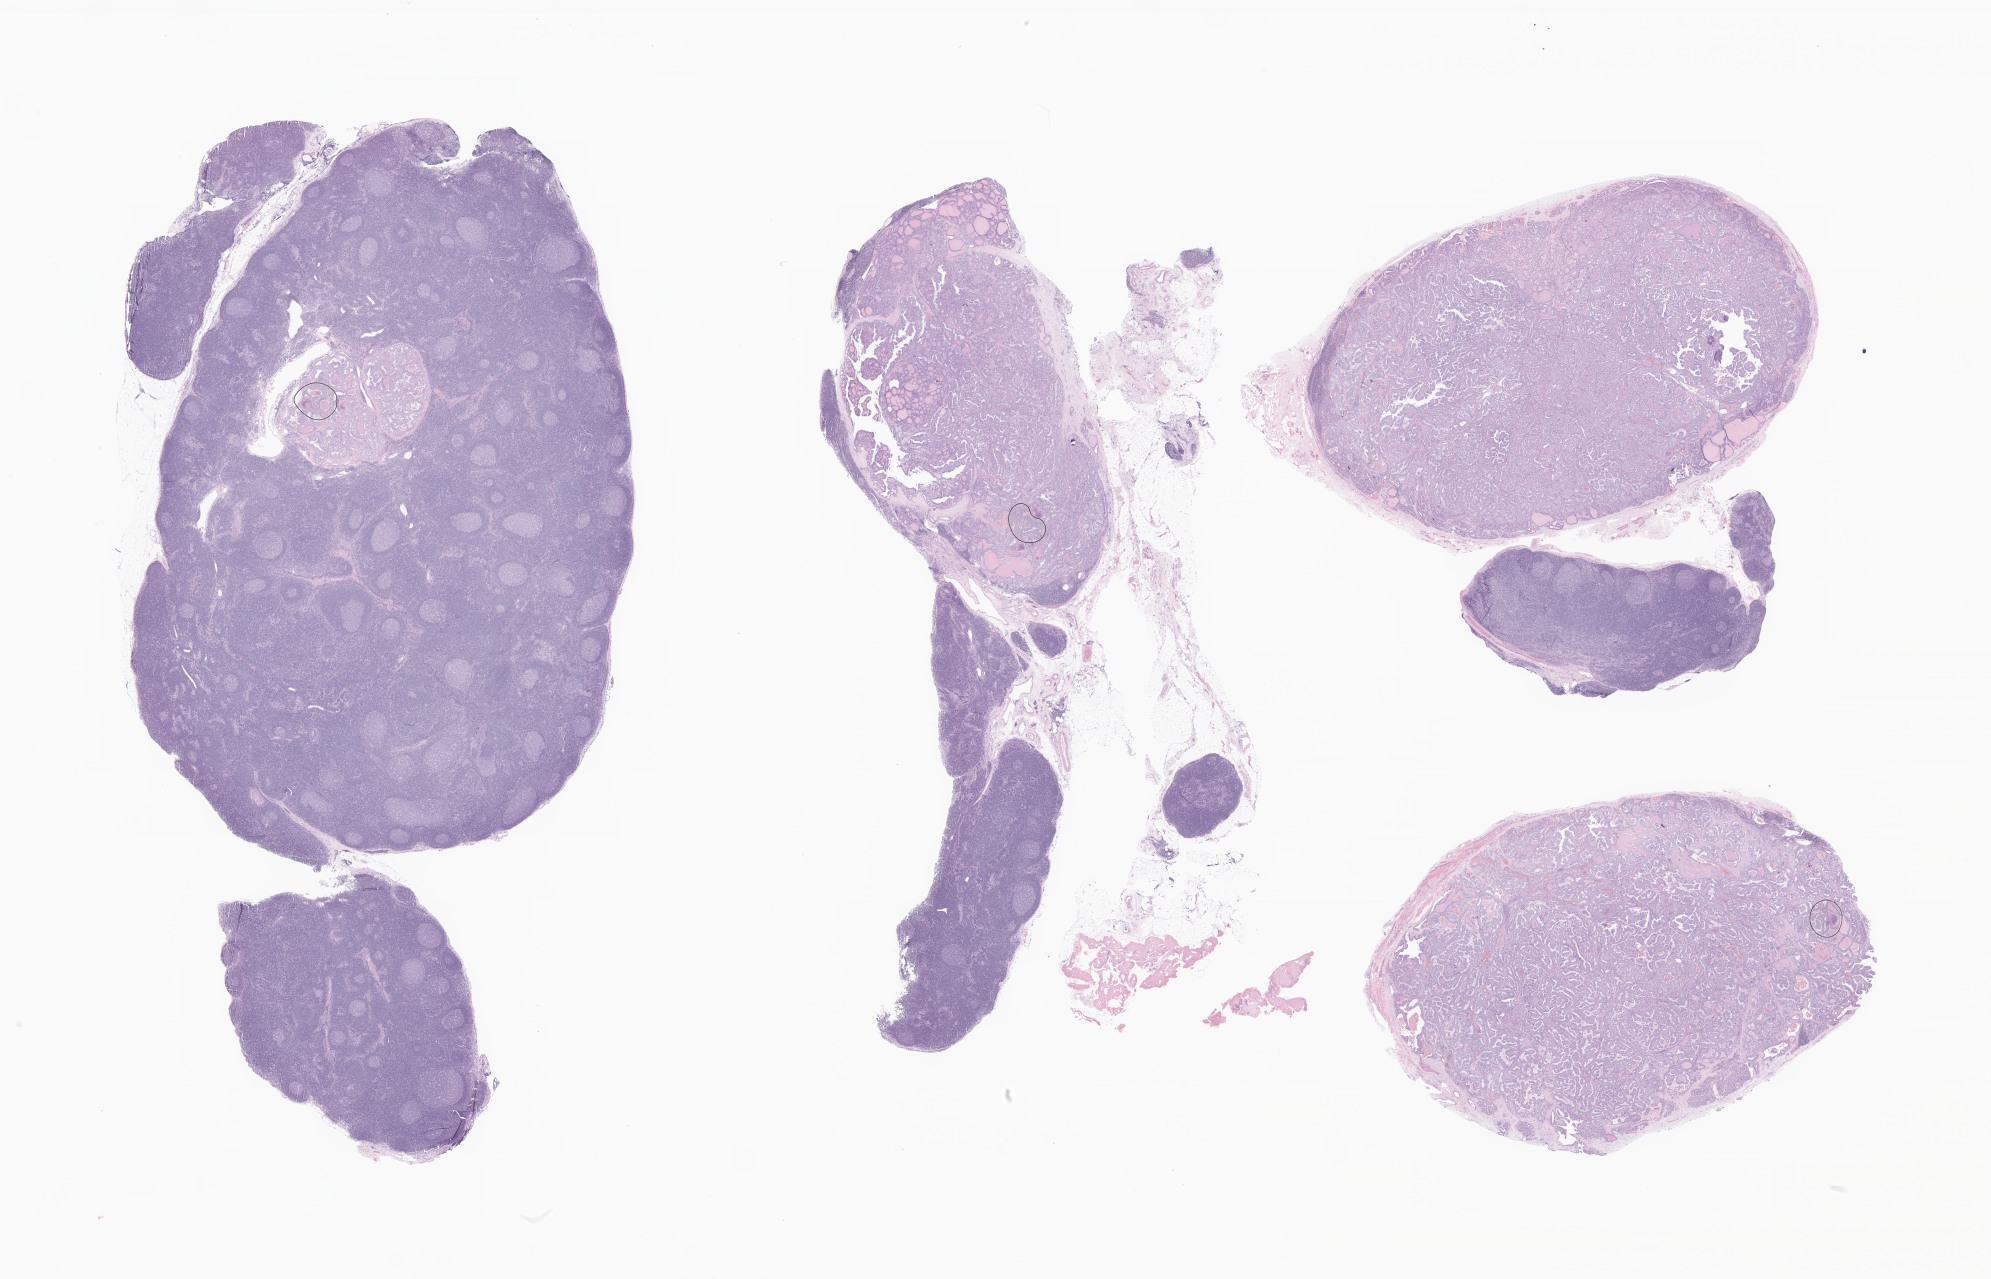
Whole-slide image, hematoxylin and eosin (H&E) stain of tumor tissue from the thyroid — low-resolution overview of the scanned area, about 33.6 x 21.6 mm; formalin-fixed paraffin-embedded section. Male patient, age 138 months.
* diagnosis (ICD-O-3 morphology term): Papillary adenocarcinoma, NOS